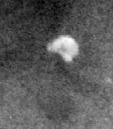
Region of interest cut from a scanned film mammogram (one marked finding), right breast, MLO view.
- Marked abnormality: calcifications, morphology round and regular / lucent center / punctate, distribution diffusely scattered; BI-RADS assessment category 2; benign without callback (not worked up further).